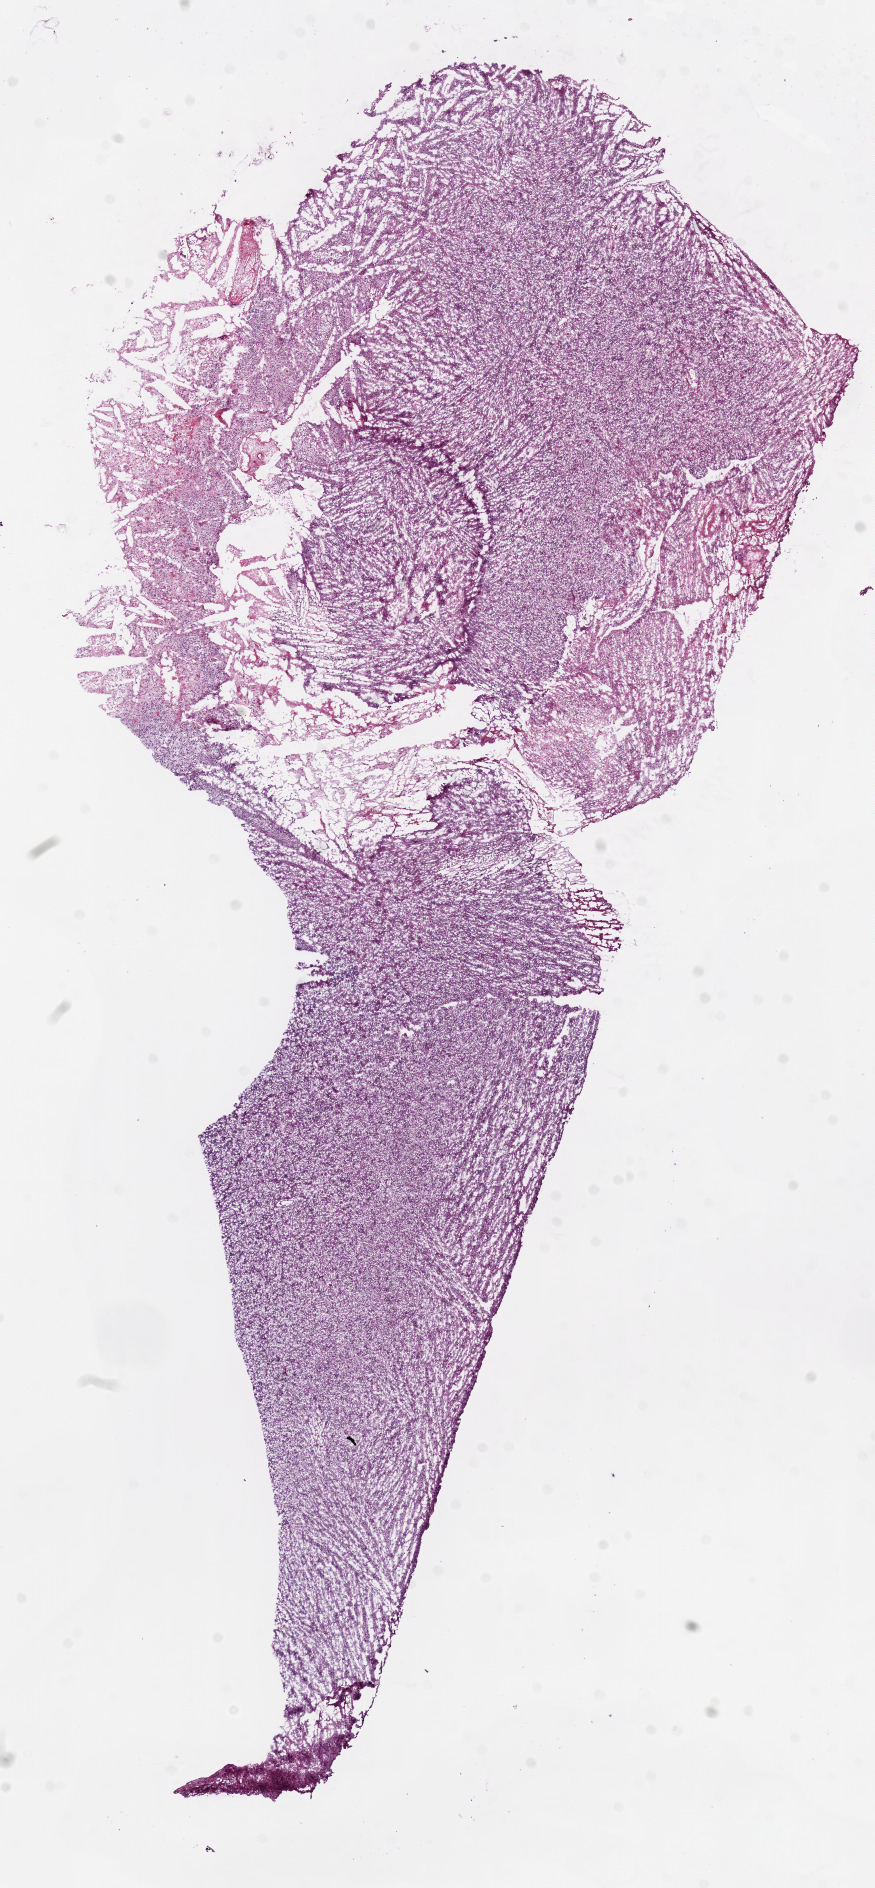
Digitized H&E-stained tissue section (whole slide) — a low-resolution overview of the entire scanned area, about 7.0 x 15.1 mm (slide scanned at 20x); frozen section from the bottom of the tissue portion; sample: primary tumour, brain. Patient: female, age at initial diagnosis 70 years. Slide review estimates, as recorded: tumour cells 95%, tumour nuclei 85%, normal cells 0%, stromal cells 0%, necrosis 5%.
Diagnosis: Glioblastoma.